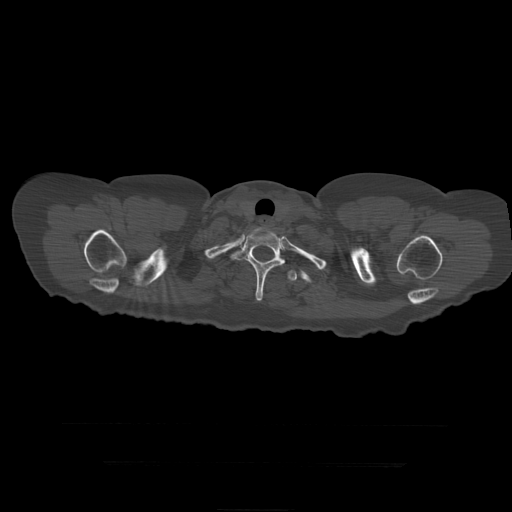
CT including the spine, one axial slice; position 376 of 399 along the scan axis; reconstruction kernel STANDARD; bone window (W 1800 / L 400 HU); 1.25 mm slice thickness; 512 × 512 image matrix, field of view 450 × 450 mm. Patient age 41 years. Case-level facts recorded for this patient, not image findings: primary cancer: breast.
Structures marked on this image (semi-automatically segmented with operator editing):
- T1 vertebra: bounding box [x1, y1, x2, y2] px = [251, 227, 270, 234]
- T2 vertebra: [231, 231, 286, 301]
- T3 vertebra: [288, 270, 298, 281]